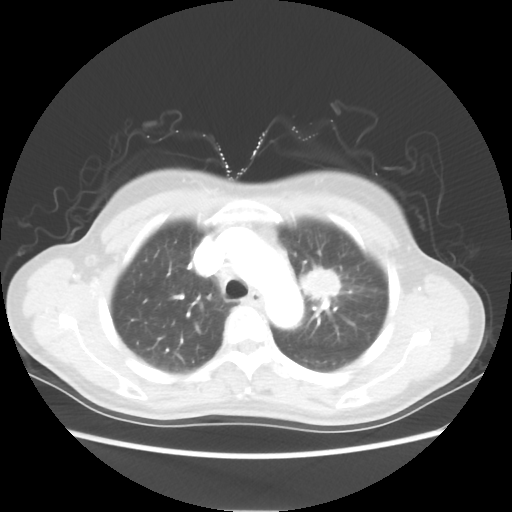
Chest CT, one axial slice; slice 40 of 54 in the series (ordered by position); reconstruction kernel STANDARD; 80 kVp; lung window (W 1500 / L -600 HU); 5 mm slice thickness; 512 × 512 image matrix, field of view 360 × 360 mm. Female patient, age 53 years. Case-level facts recorded for this patient, not image findings: clinical TNM (as recorded): T1c N0 M0.
Outlined on this slice (rectangle marked by the reading radiologist):
- lung tumour (recorded histology: adenocarcinoma): bounding box (x1, y1, x2, y2) in pixels: (291, 252, 346, 309)
- lung tumour (recorded histology: adenocarcinoma): (293, 260, 342, 304)